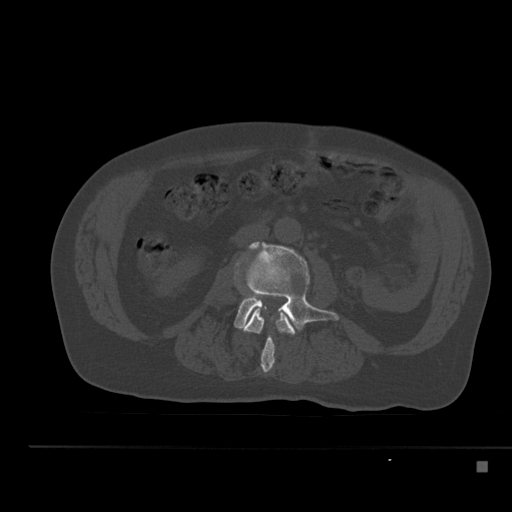
CT including the spine, one axial slice. Slice 171 of 517 in the series (ordered by position). Reconstruction kernel Br40s. Bone window (W 1800 / L 400 HU). 512 × 512 image matrix. Male patient, age 70 years. Case-level facts recorded for this patient, not image findings: primary cancer: renal.
Structures marked on this image (semi-automatic segmentation, software-assisted and operator-edited):
- L2 vertebra: box from (x=241, y=310) to (x=295, y=373) px
- L3 vertebra: (x=234, y=240)–(x=340, y=331)